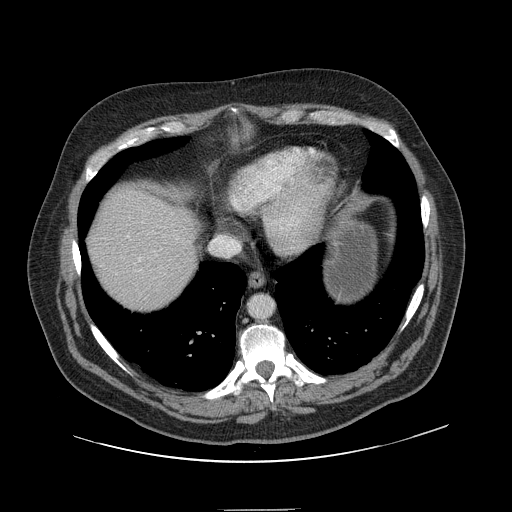
Contrast-enhanced abdominal CT, one axial slice; slice 134 of 154 in the series (ordered by position); 120 kVp; intravenous contrast given; soft-tissue window (W 400 / L 40 HU); 2.5 mm slice thickness; 512 × 512 image matrix, field of view 451 × 451 mm. Male patient, age 61 years. From the clinical record (not read from this slice): diagnosis: colorectal cancer liver metastases, imaged before liver resection; multiple liver metastases: yes; largest metastasis: 2.6 cm.
Outlined on this slice (outlined manually by an expert reader):
- liver: bounding box <91,190,196,311> (left, top, right, bottom; pixels)
- planned liver remnant (the part of the liver to remain after resection): <90,190,196,311>
- portal vein (with intrahepatic branches): <128,217,141,261>